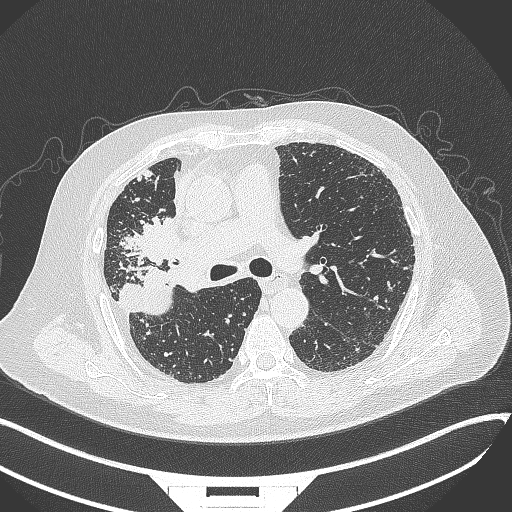
Chest CT, one axial slice. Position 213 of 384 along the scan axis. Reconstruction kernel B70f. 120 kVp. Lung window (W 1500 / L -600 HU). 1 mm slice thickness. 512 × 512 image matrix, field of view 400 × 400 mm. Patient: male, 69 years. Case-level facts recorded for this patient, not image findings: clinical TNM (as recorded): T4 N3 M1.
Structures marked on this image (rectangle marked by the reading radiologist):
- lung tumour (recorded histology: adenocarcinoma): bounding box <115,215,187,270> (left, top, right, bottom; pixels)